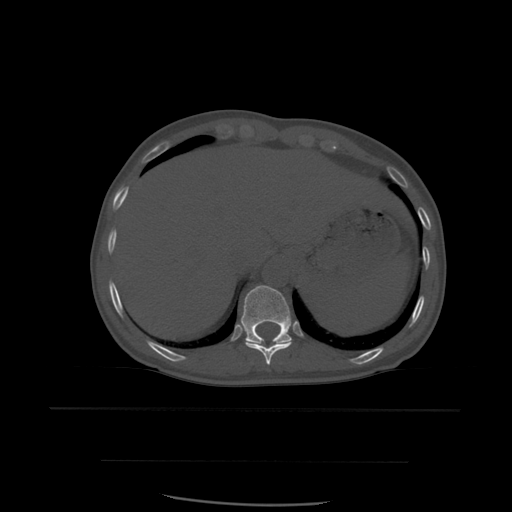
CT including the spine, one axial slice. Slice 305 of 574 in the series (ordered by position). Bone window (W 1800 / L 400 HU). 1.25 mm slice thickness. 512 × 512 image matrix. Patient age 48 years. From the clinical record (not read from this slice): primary cancer: lung.
Structures marked on this image (semi-automatic segmentation, software-assisted and operator-edited):
- T10 vertebra: bounding box (x1, y1, x2, y2) in pixels: (245, 342, 292, 366)
- T11 vertebra: (241, 286, 294, 345)